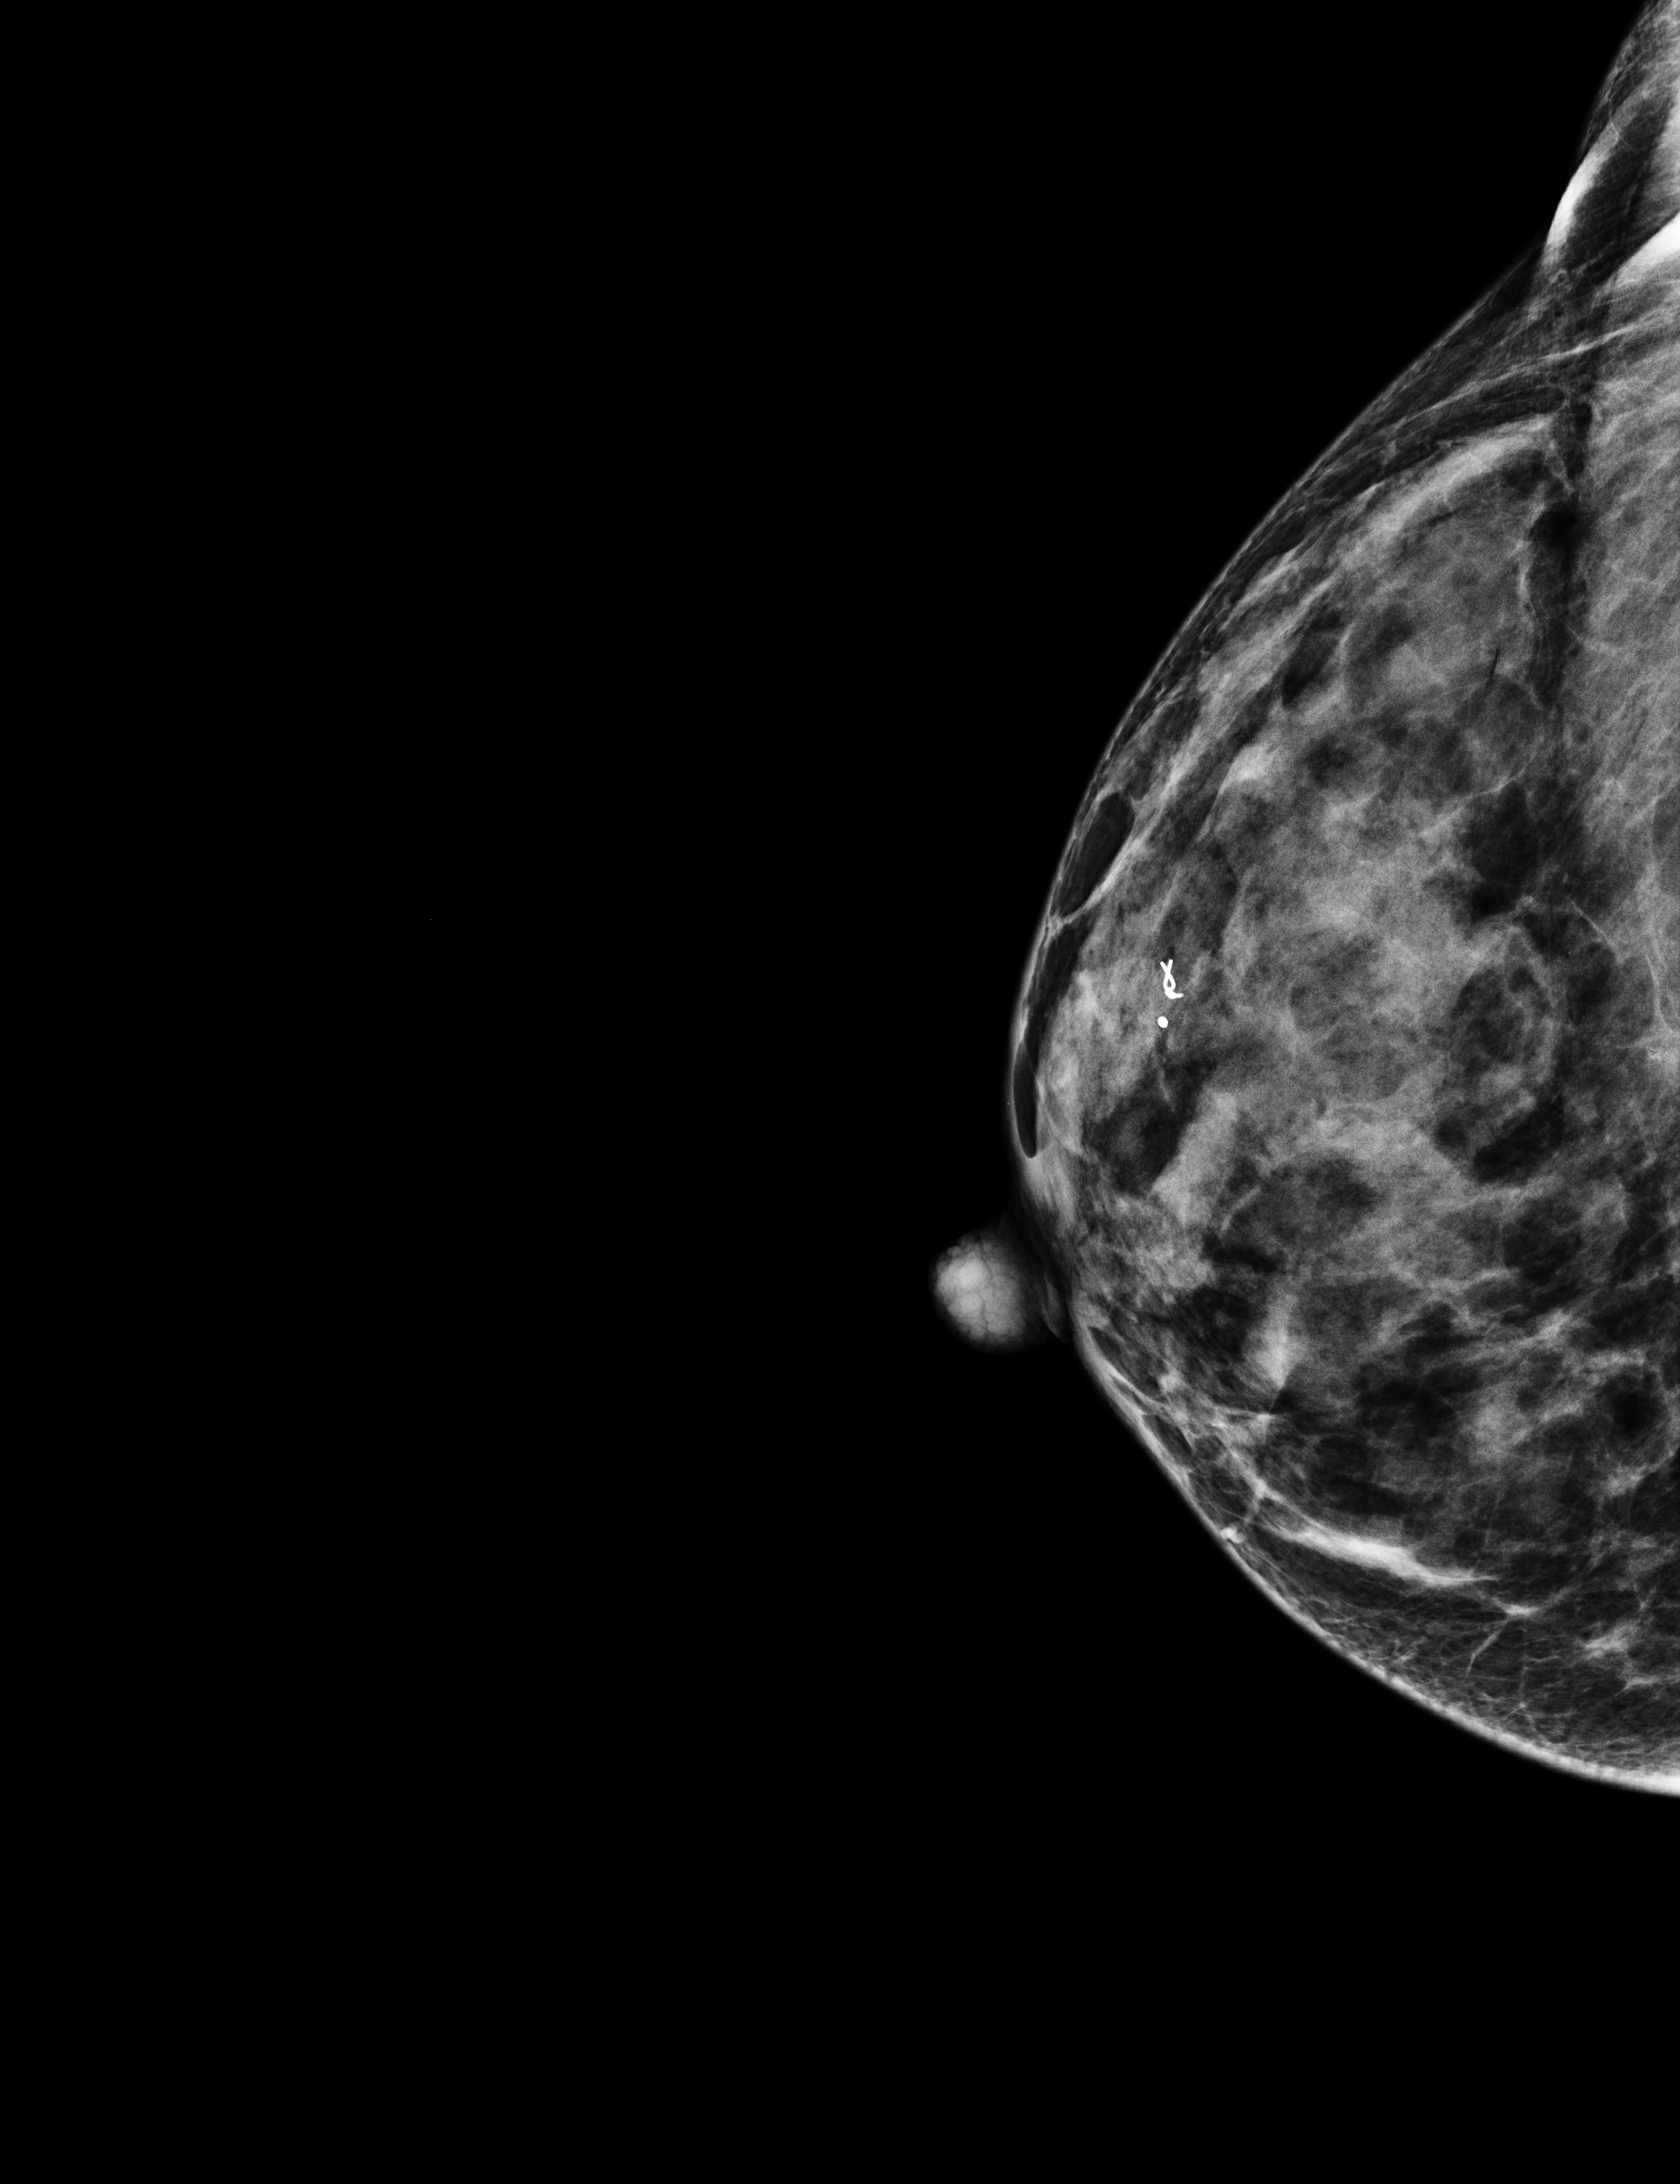
Screening examination, compressed breast thickness 35 mm. Patient: female, 54 years.
Image type: full-field digital mammogram. Breast: right. Projection: laterally exaggerated craniocaudal (XCCL) view.